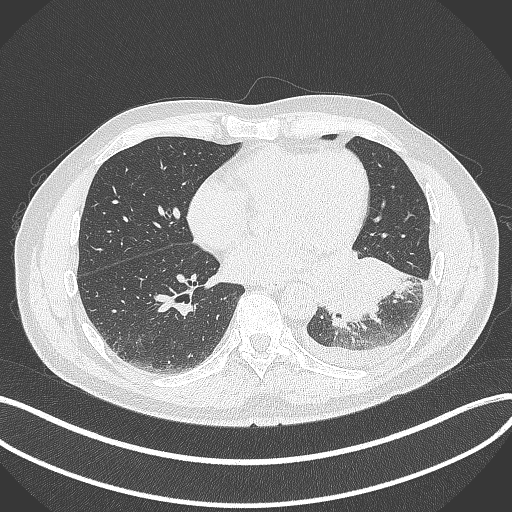
Chest CT, one axial slice. Slice 144 of 342 in the series (ordered by position). Reconstruction kernel B70f. 120 kVp. Lung window (W 1500 / L -600 HU). 1 mm slice thickness. 512 × 512 image matrix, field of view 400 × 400 mm. Male patient, age 58 years. From the clinical record (not read from this slice): clinical TNM (as recorded): T3 N1 M1b; histopathological grade: G3.
Structures marked on this image (bounding box drawn by a radiologist):
- lung tumour (recorded histology: small cell carcinoma): box from (x=308, y=246) to (x=414, y=330) px